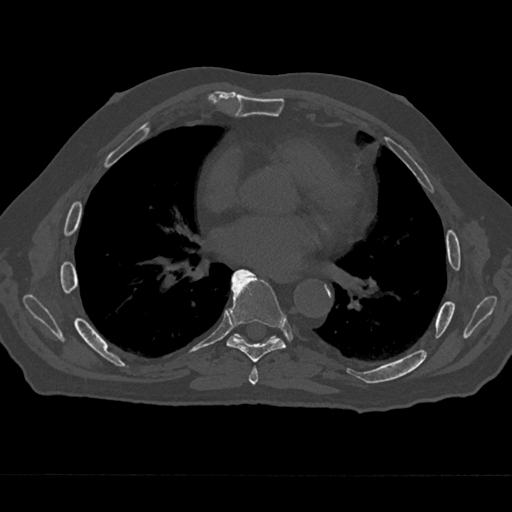
CT including the spine, one axial slice. Slice 362 of 797 in the series (ordered by position). Reconstruction kernel Br40s/3. 120 kVp. Bone window (W 1800 / L 400 HU). 0.5 mm slice thickness. 512 × 512 image matrix. Male patient, age 75 years. From the clinical record (not read from this slice): primary cancer: renal; vertebrae with lytic lesions (as recorded): T4.
Annotated regions visible in this slice (semi-automatic segmentation, software-assisted and operator-edited):
- T6 vertebra: bounding box [x1, y1, x2, y2] px = [249, 366, 259, 385]
- T7 vertebra: [227, 269, 286, 362]
- T8 vertebra: [234, 334, 276, 341]